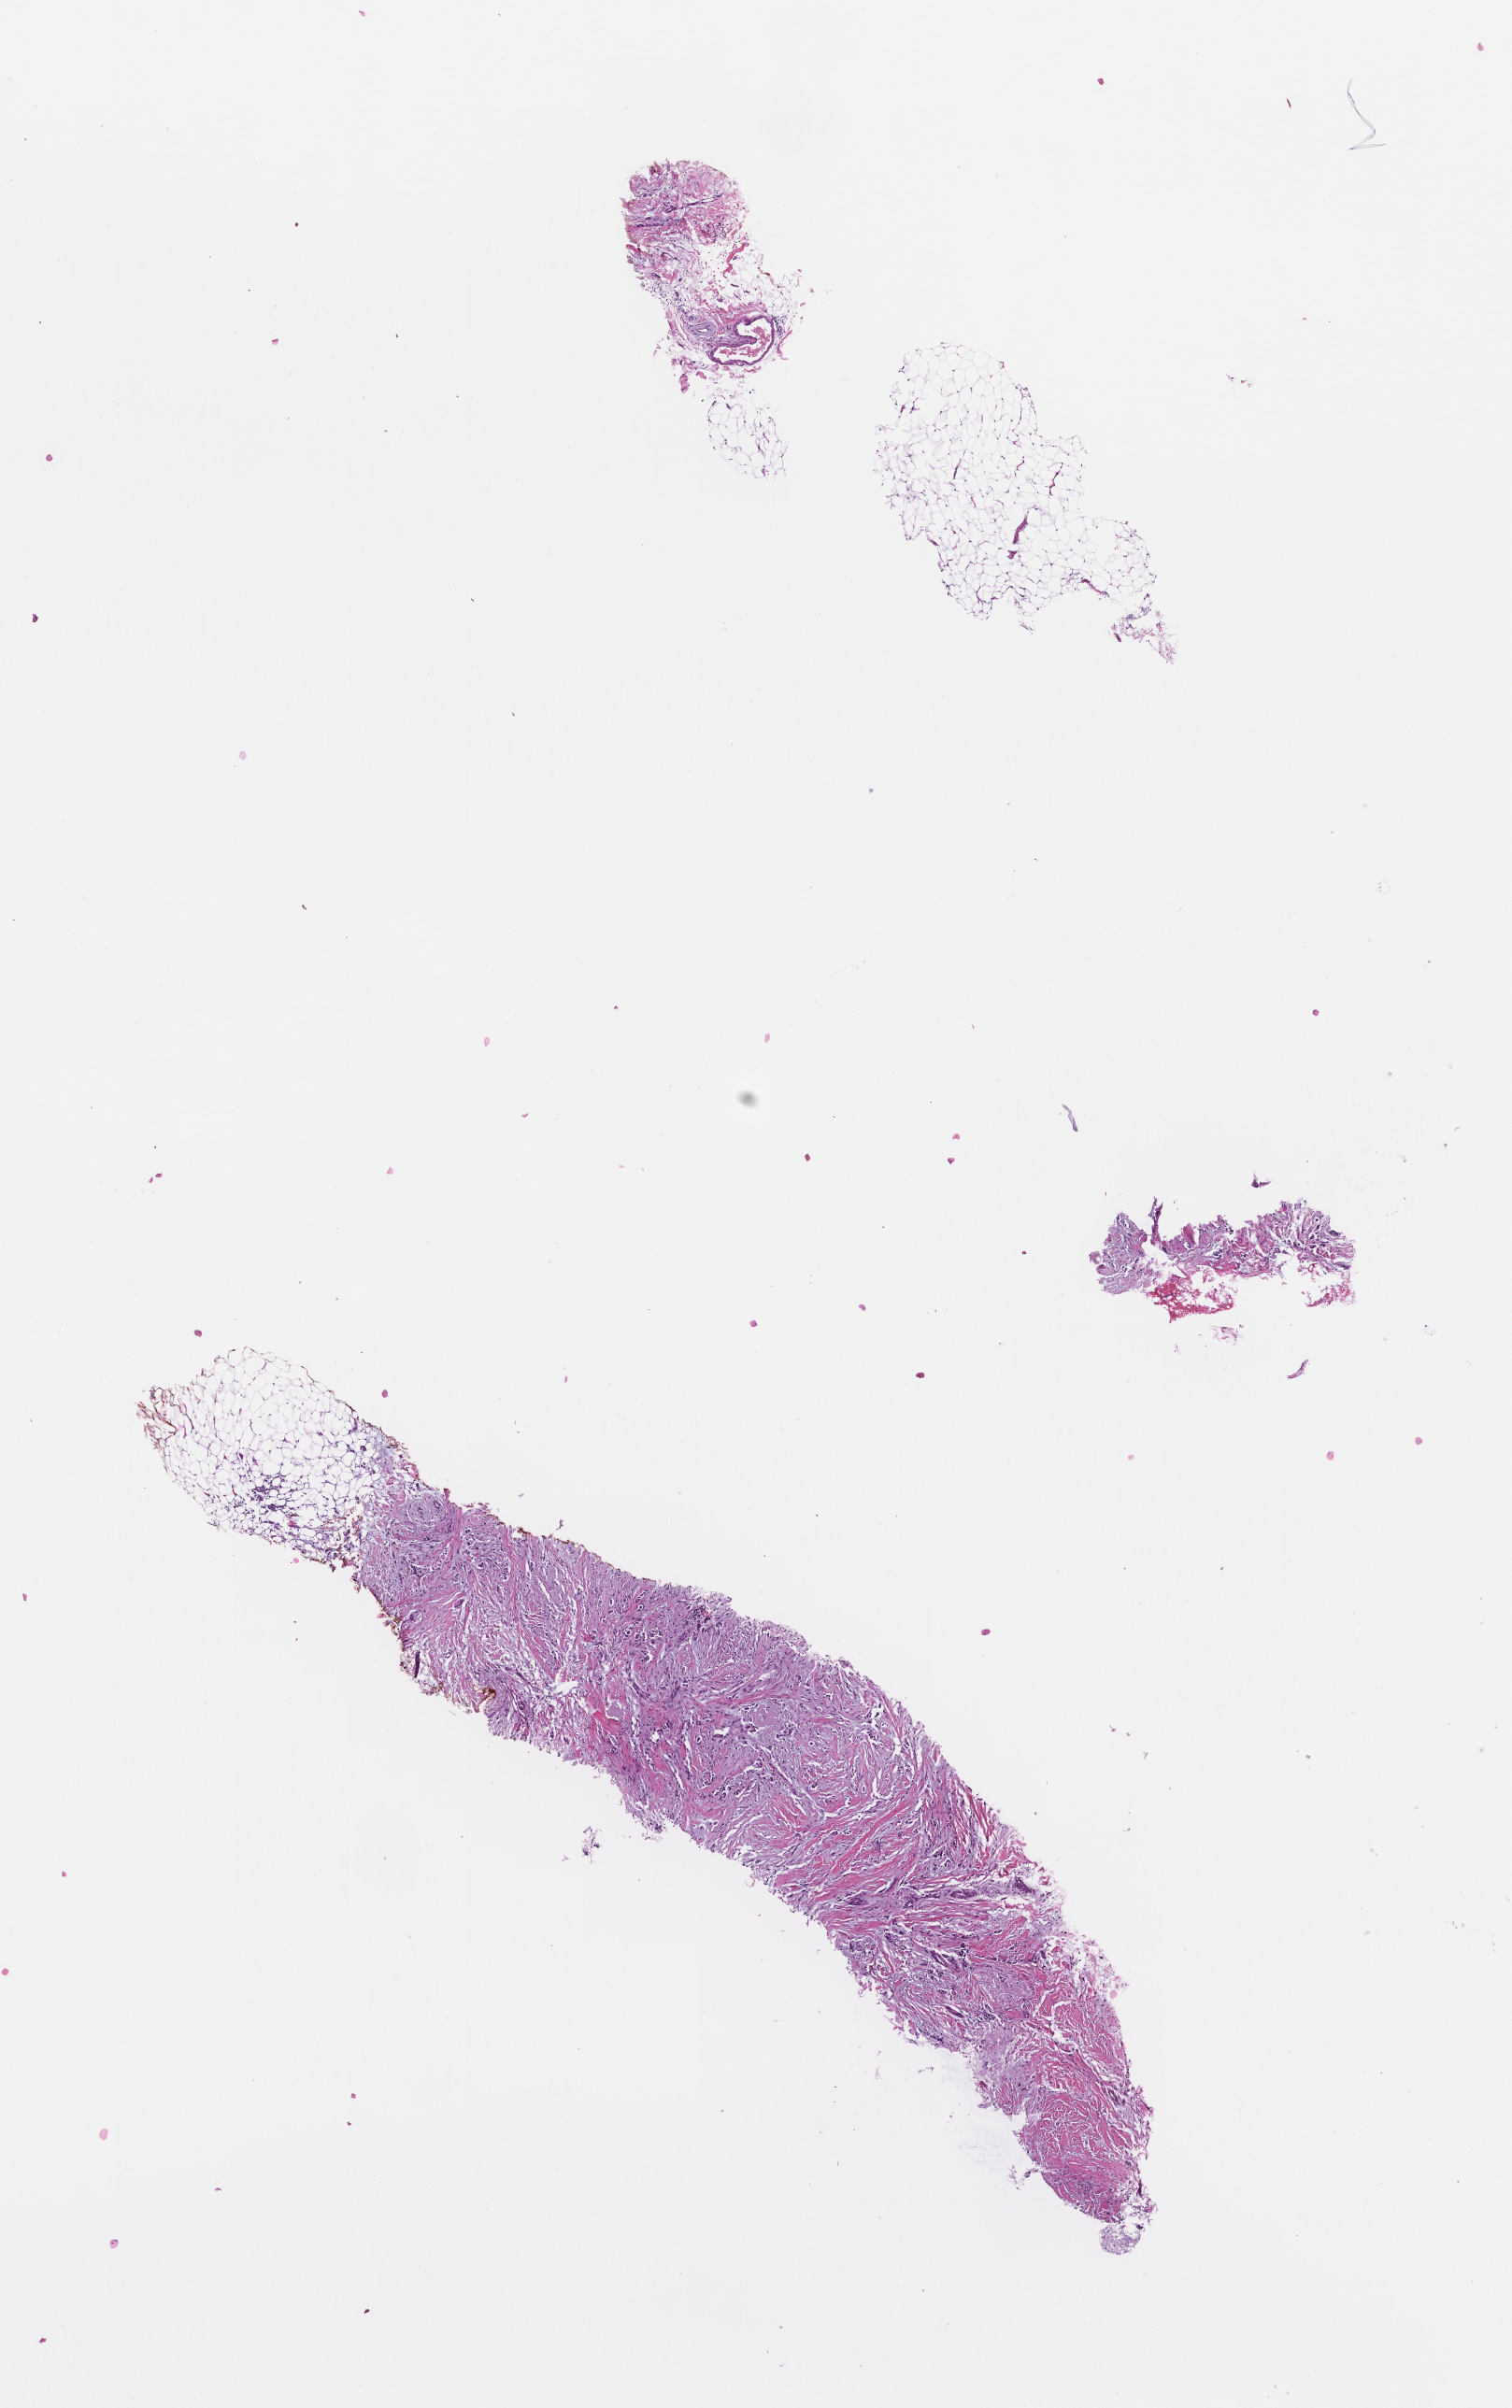
Whole-slide image, hematoxylin and eosin (H&E) stain — whole scanned area (about 6.5 x 10.4 mm) shown as a low-resolution overview; formalin-fixed paraffin-embedded section; archival tissue. Patient: female.
This section: metastasis (sampled organ not recorded). Patient diagnosis (primary): Invasive Breast Carcinoma.